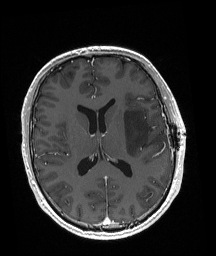
Brain MRI from a brain-tumour surgery series, one axial slice. Position 88 of 192 along the scan axis. T1-weighted post-contrast. 1 mm slice thickness. 216 × 256 image matrix, field of view 211 × 250 mm. From the clinical record (not read from this slice): histopathology: Astrocytoma; WHO grade: 3; IDH mutation: yes; tumour location: Left Posterior Frontal.
Annotated regions visible in this slice (expert manual segmentation):
- tumour: bounding box (x1, y1, x2, y2) in pixels: (123, 109, 163, 157)